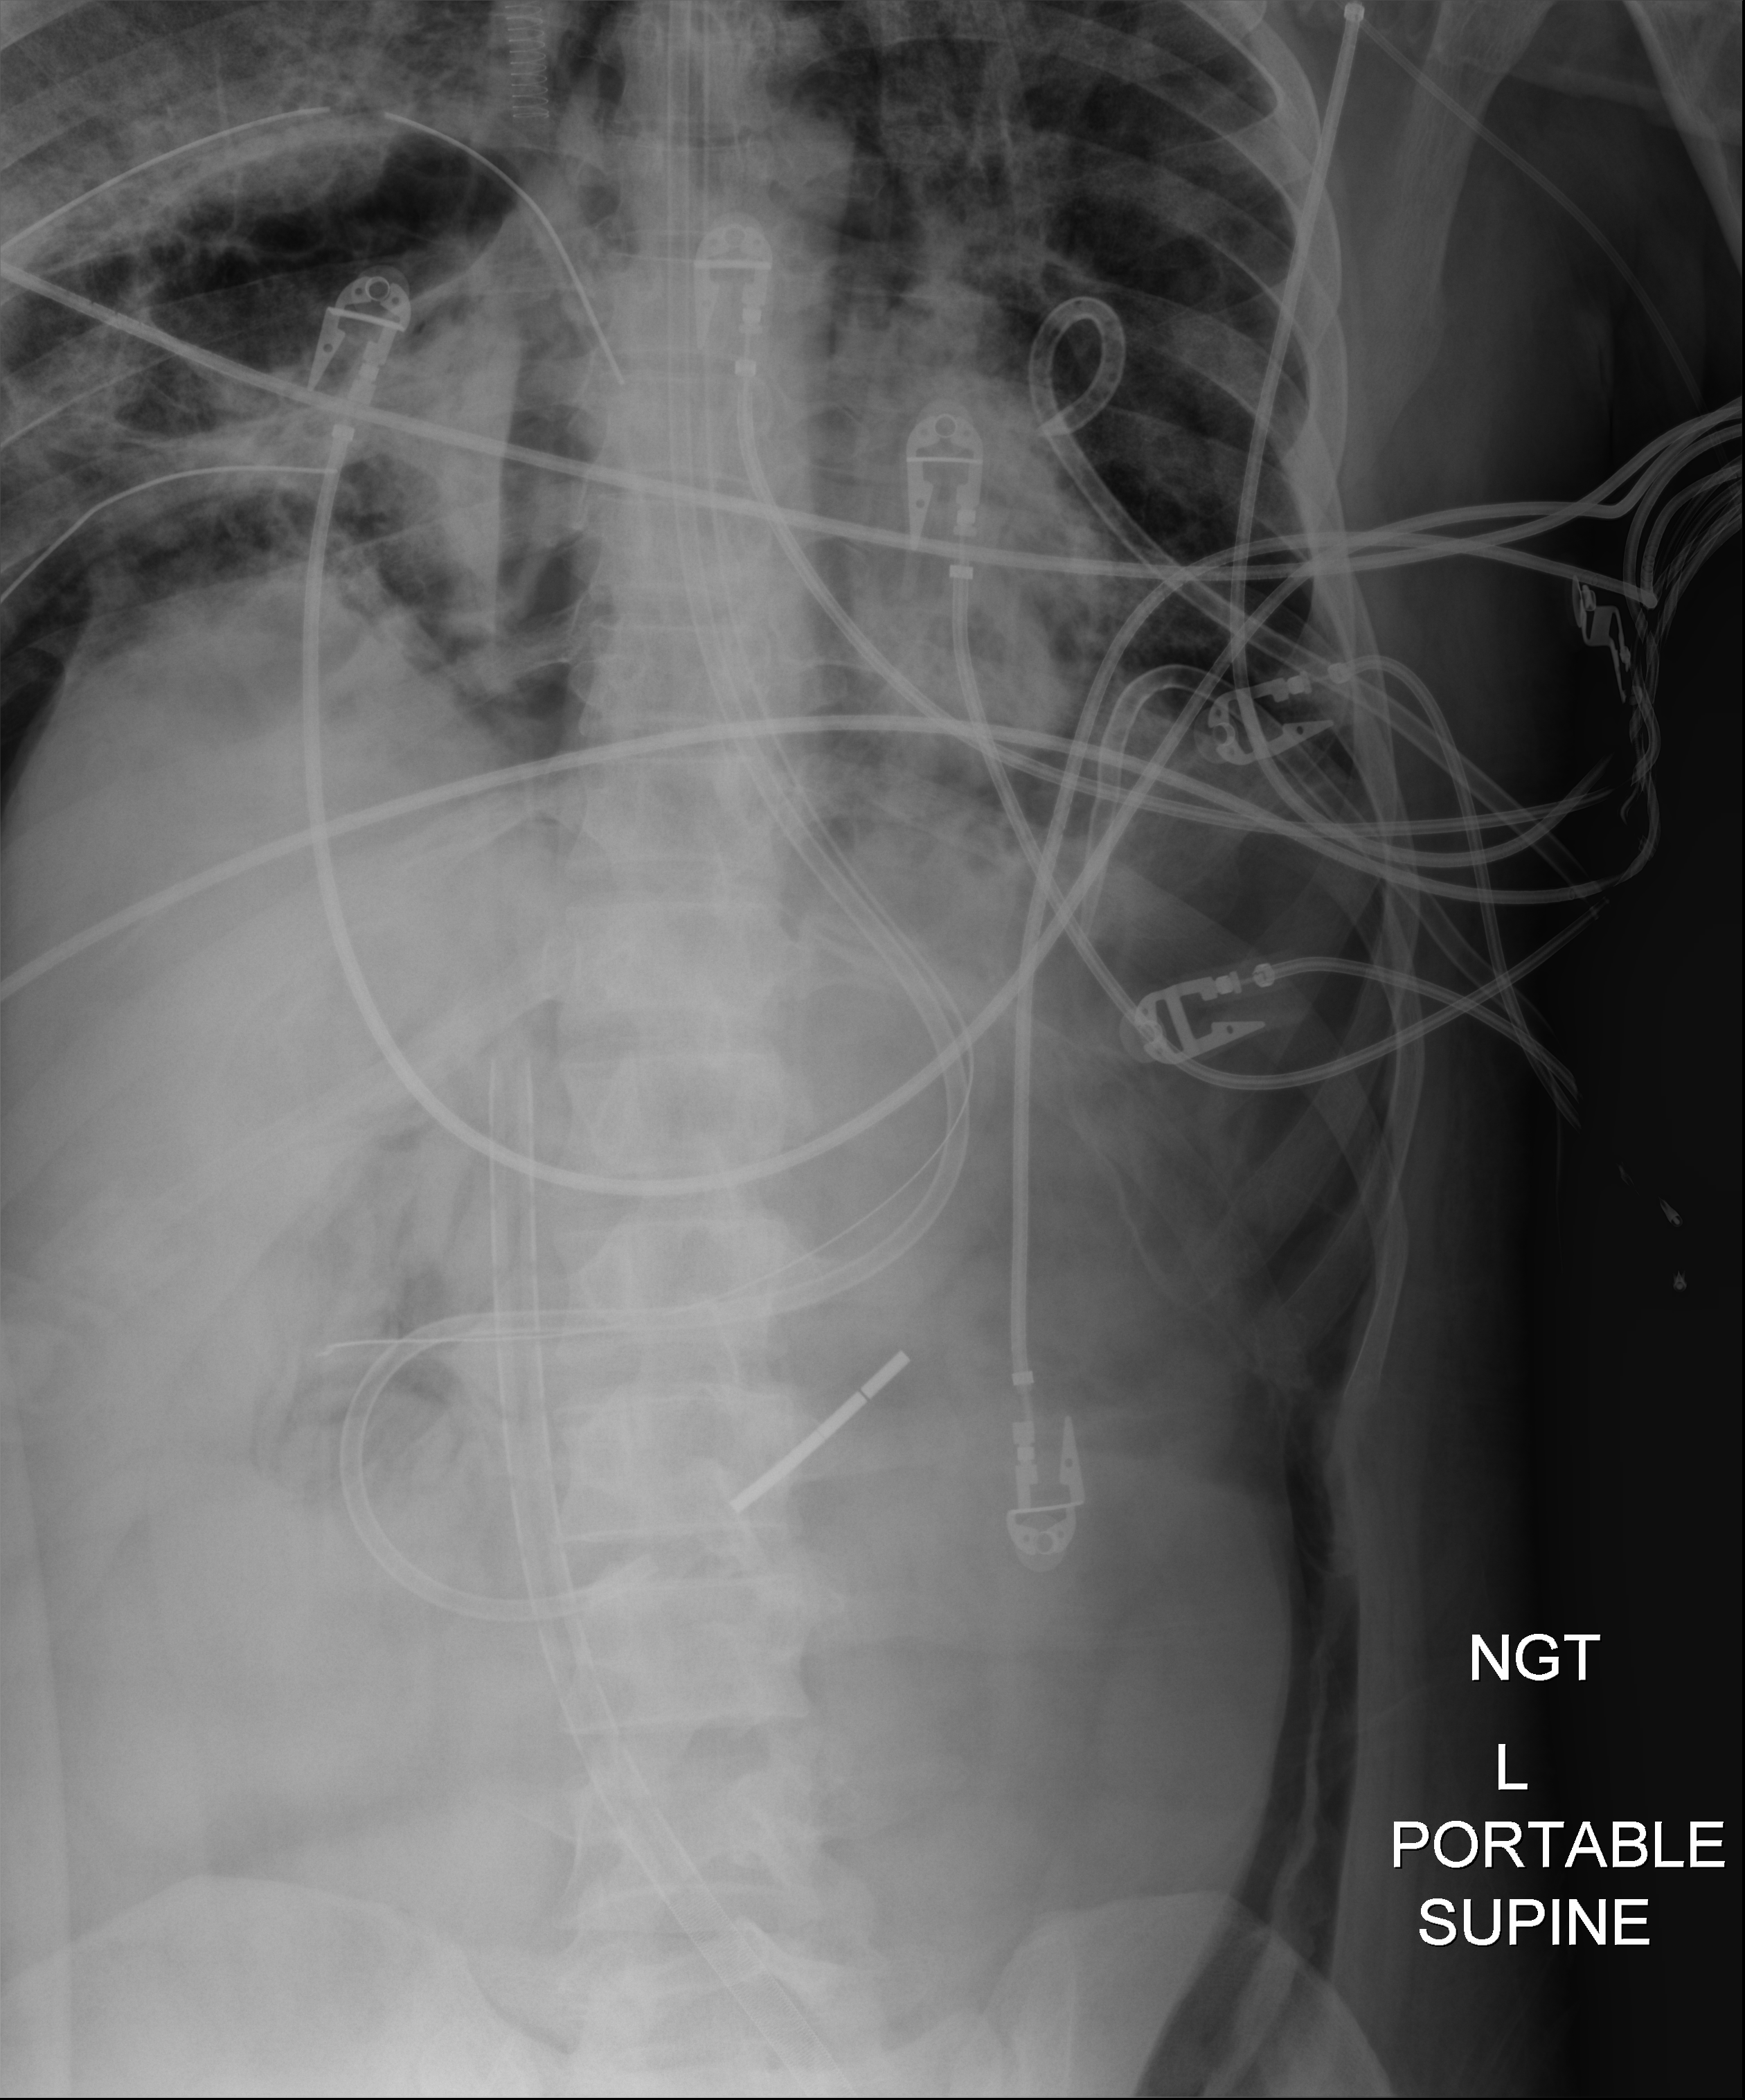
Bedside abdomen radiograph (digital radiography); anteroposterior (AP) projection. Patient hospitalised with COVID-19, aged 18–59 years.
From the hospital-stay record, not from the radiograph (when in the stay this image was taken is not recorded): smoking status (admission record): never; admitted to intensive care during this hospital stay: yes.